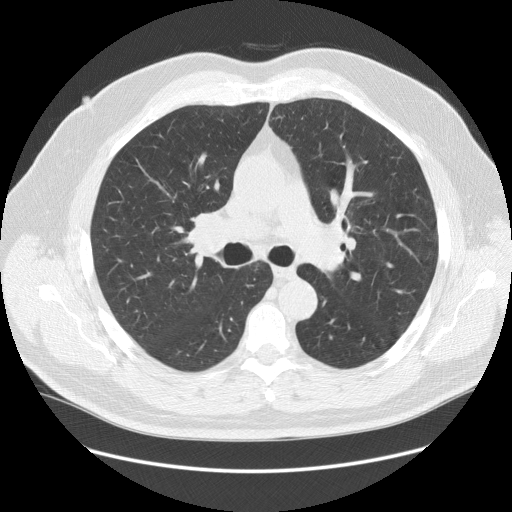
Axial slice from a low-dose chest CT screening exam. Baseline screening round. Lung window (W 1500 / L -600 HU). Slice 53 of 140 in the series. Male, age 64 years at enrolment. Former smoker at enrolment.
Expert-annotated lung lesion, bounding box (x1, y1, x2, y2) in pixels: (180, 200, 250, 270). Screening reader's record for this exam (one nodule recorded; not confirmed to be the boxed lesion): non-calcified nodule or mass ≥4 mm, right lower lobe, 7 × 5 mm, smooth margins, soft tissue attenuation. Official screen result: positive, change unspecified: nodule(s) >= 4 mm or enlarging nodule(s), mass(es), or other non-specific abnormalities suspicious for lung cancer. Later outcome: lung cancer diagnosed 456 days after this screen (after the second annual screen) — adenocarcinoma, NOS, right upper lobe, poorly differentiated (G3), stage IB (AJCC 6th edition), 37 mm at pathology.